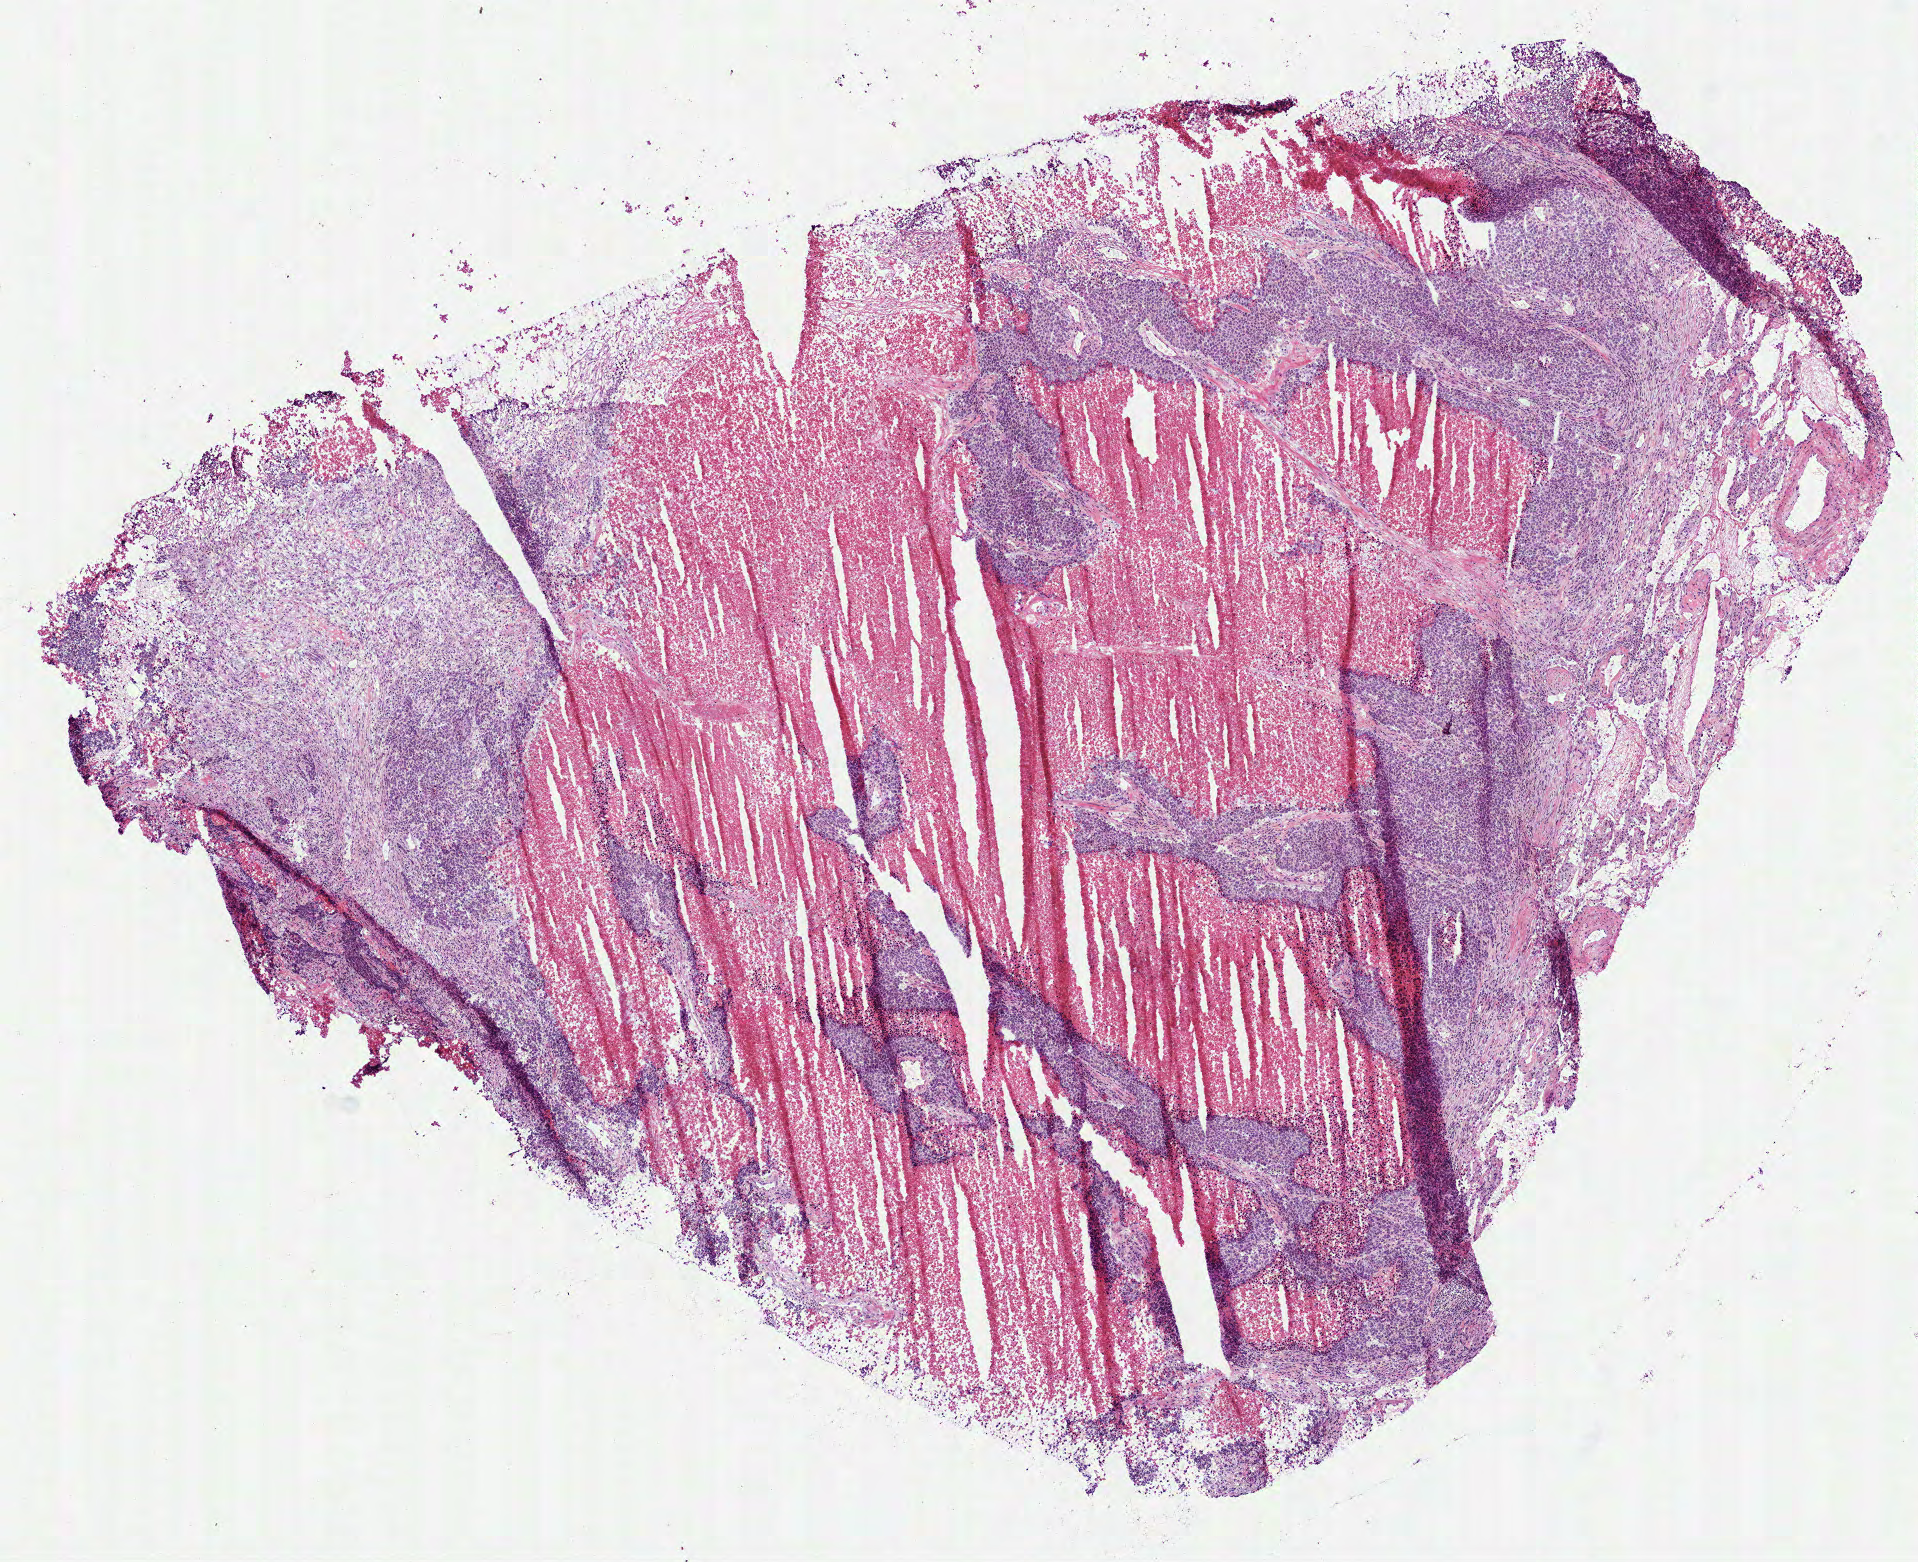
Whole-slide histology image, Hematoxylin and eosin (H&E) stained — low-resolution overview of the scanned area, about 7.7 x 6.3 mm (acquisition: 40x scan). Frozen section from the bottom of the tissue portion. Lung, primary tumour sample. Female, age 76 years at initial diagnosis. Composition of this section per pathologist review: tumour cells 30%, tumour nuclei 70%, normal cells 0%, stromal cells 10%, necrosis 60%.
AJCC pathologic stage: IA (7th edition). Diagnosis: Adenocarcinoma, NOS (lower lobe, lung).